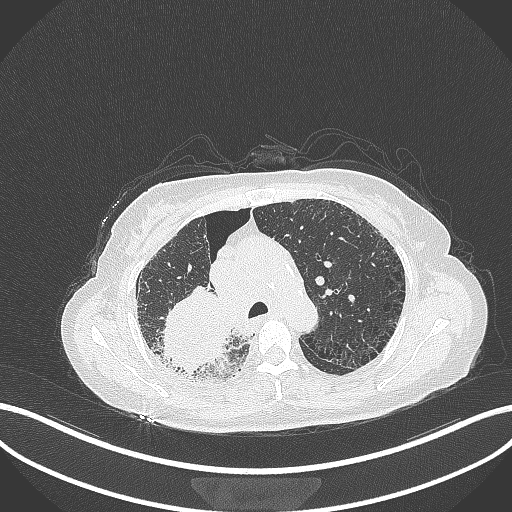
Chest CT, one axial slice. Position 240 of 408 along the scan axis. Reconstruction kernel B70f. 120 kVp. Lung window (W 1500 / L -600 HU). 512 × 512 image matrix. Patient: female, 64 years. From the clinical record (not read from this slice): clinical TNM (as recorded): T3 N3 M0.
Outlined on this slice (bounding box drawn by a radiologist):
- lung tumour (recorded histology: squamous cell carcinoma): bounding box (x1, y1, x2, y2) in pixels: (158, 278, 233, 375)